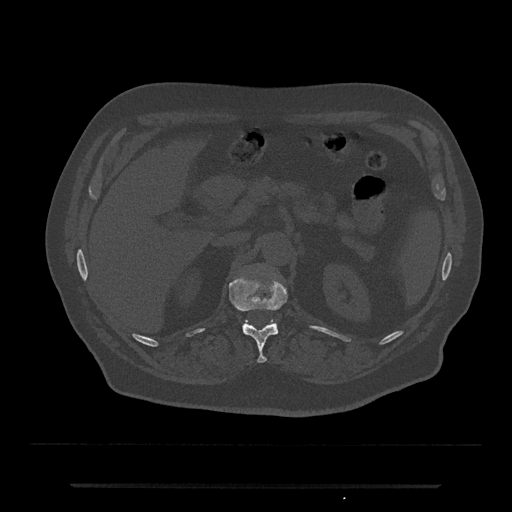
CT including the spine, one axial slice; position 582 of 797 along the scan axis; reconstruction kernel Br40s/3; bone window (W 1800 / L 400 HU); 512 × 512 image matrix, field of view 434 × 434 mm. Male patient, age 80 years. From the clinical record (not read from this slice): primary cancer: prostate; vertebrae with lytic lesions (as recorded): L1, T11.
Structures marked on this image (semi-automatic segmentation, software-assisted and operator-edited):
- L1 vertebra: bounding box [x1, y1, x2, y2] px = [244, 321, 276, 324]
- T12 vertebra: [229, 278, 288, 363]